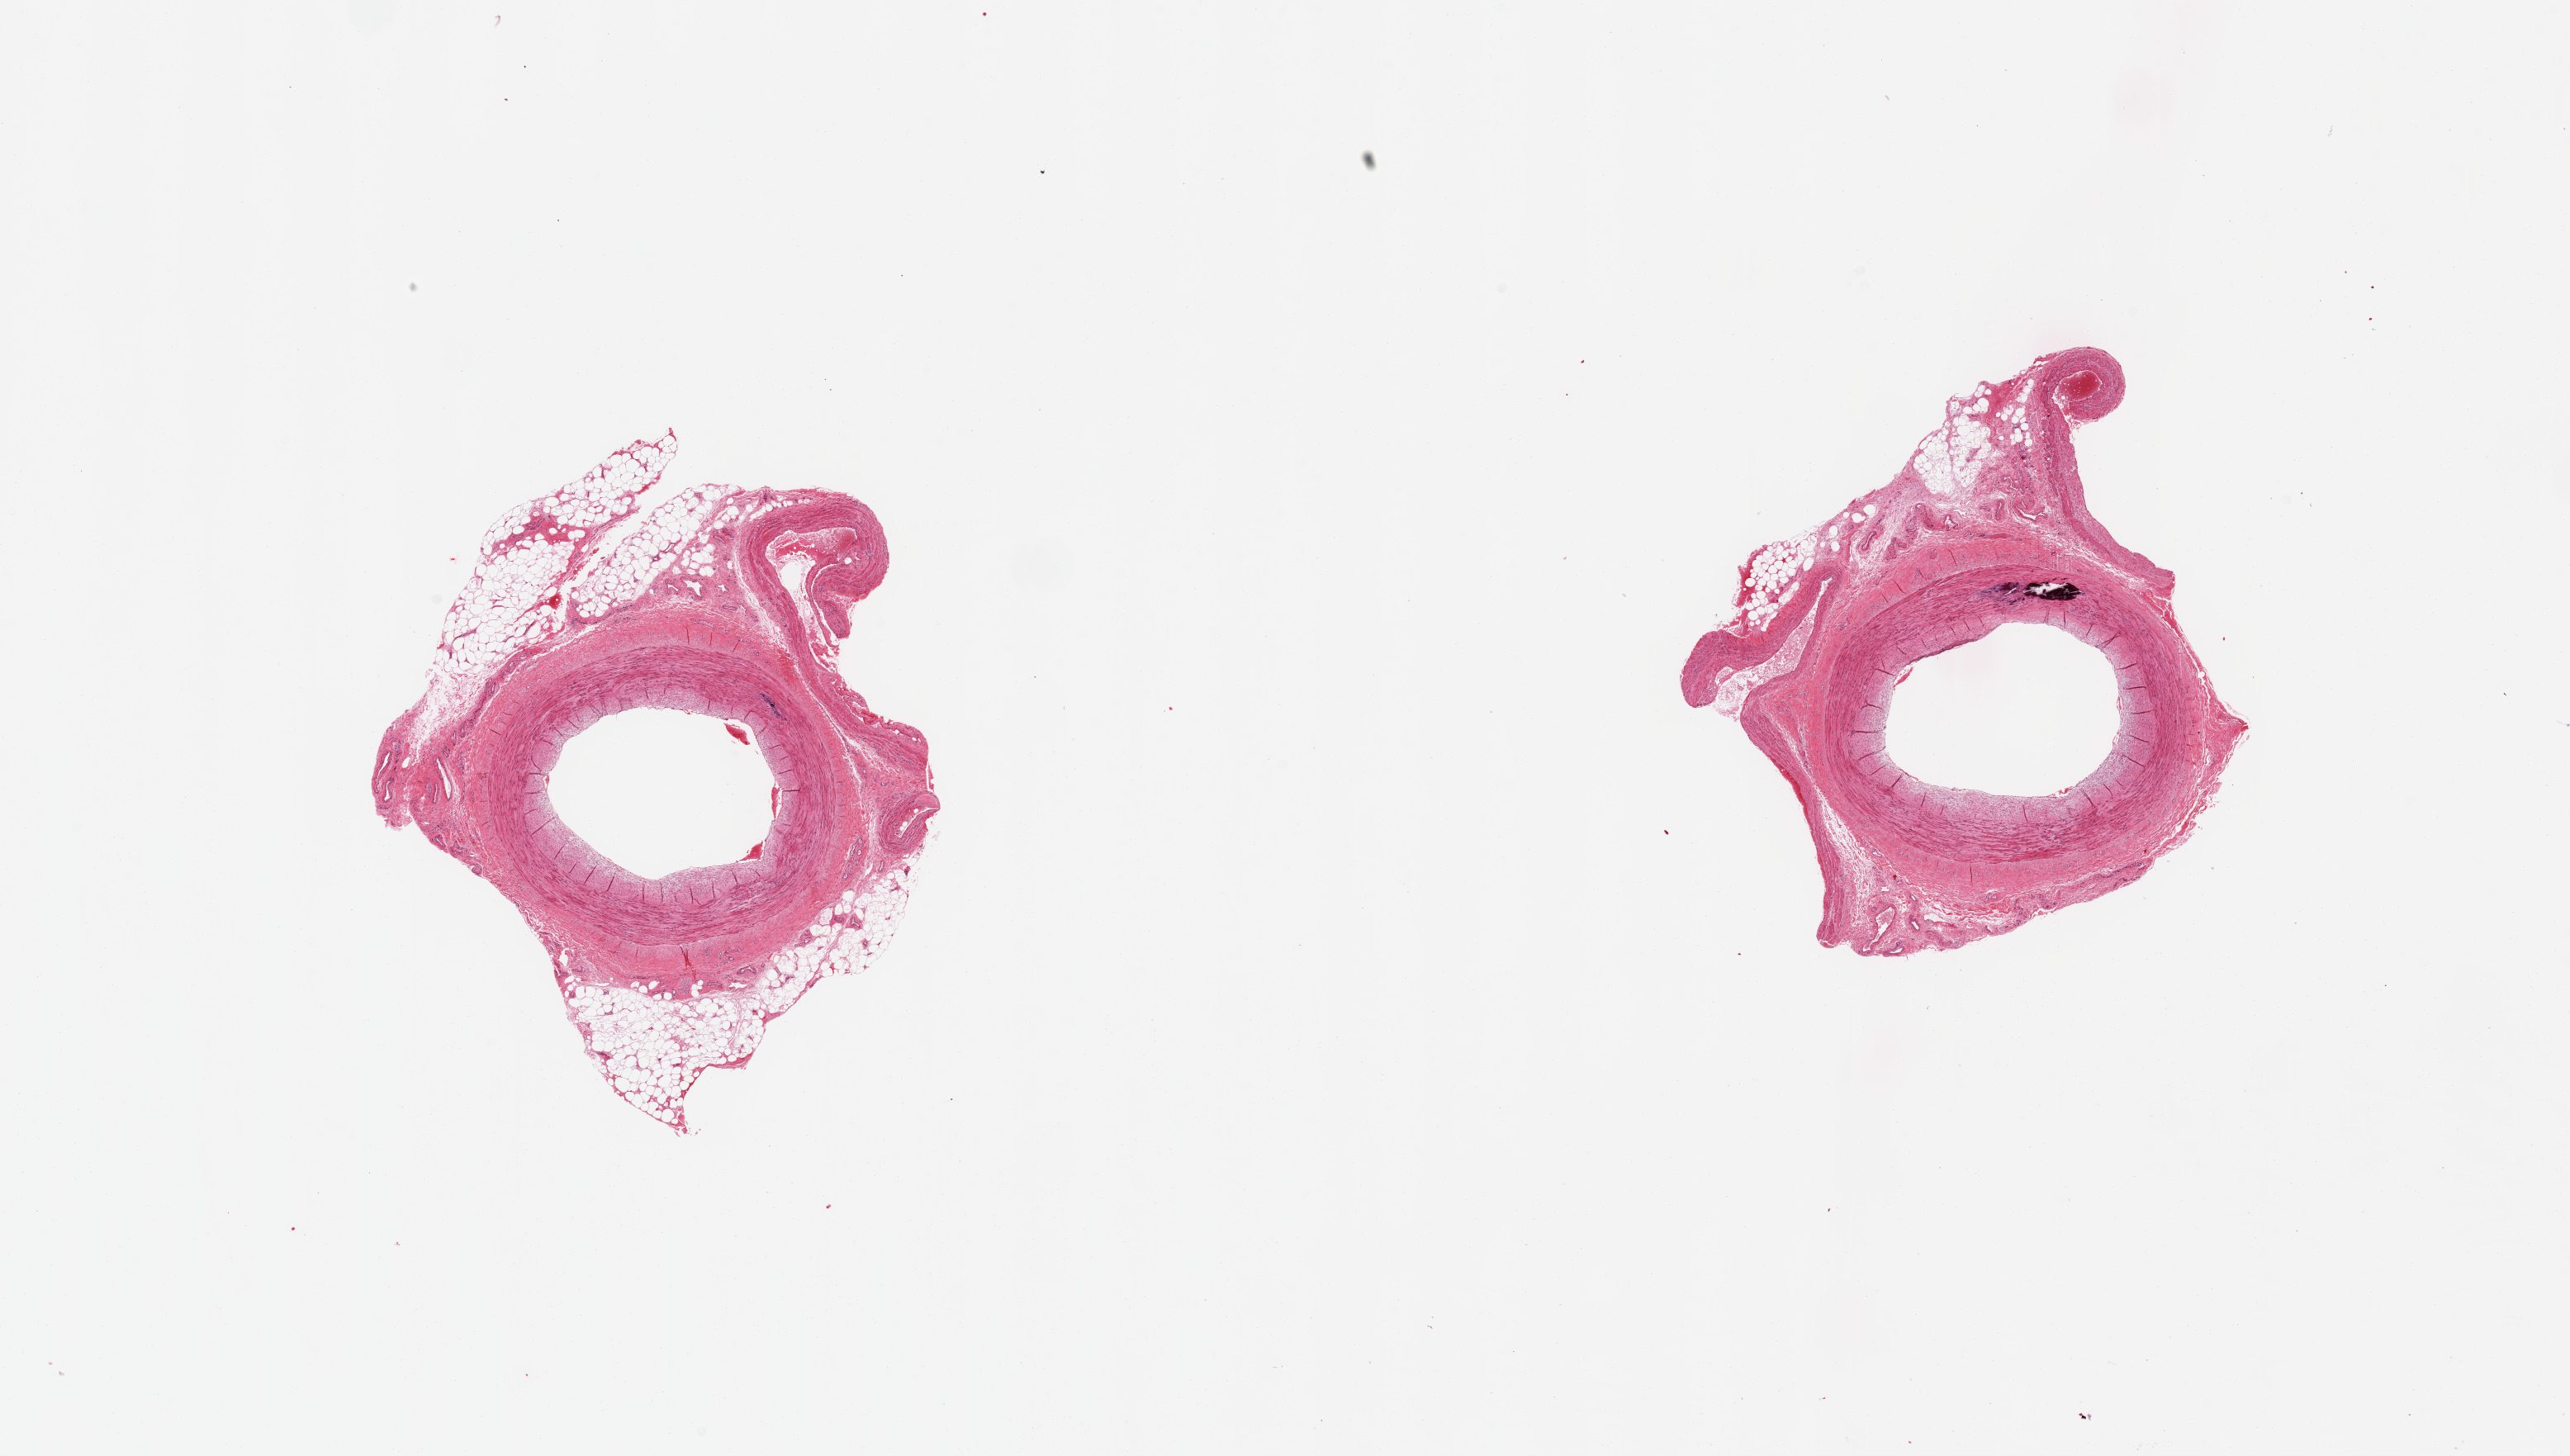
Digitized H&E-stained section, whole scanned area (about 24.6 x 13.9 mm, slide scanned at 20x) shown as a low-resolution overview, PAXgene-fixed paraffin-embedded (PFPE) section, sampled site (target tissue): tibial artery, tissue donor sample. Donor sex: male.
• review note (as recorded): 2 pieces; slight intimal sclerotic plaques; single focus of medial calcification; 20 & 40% external fat